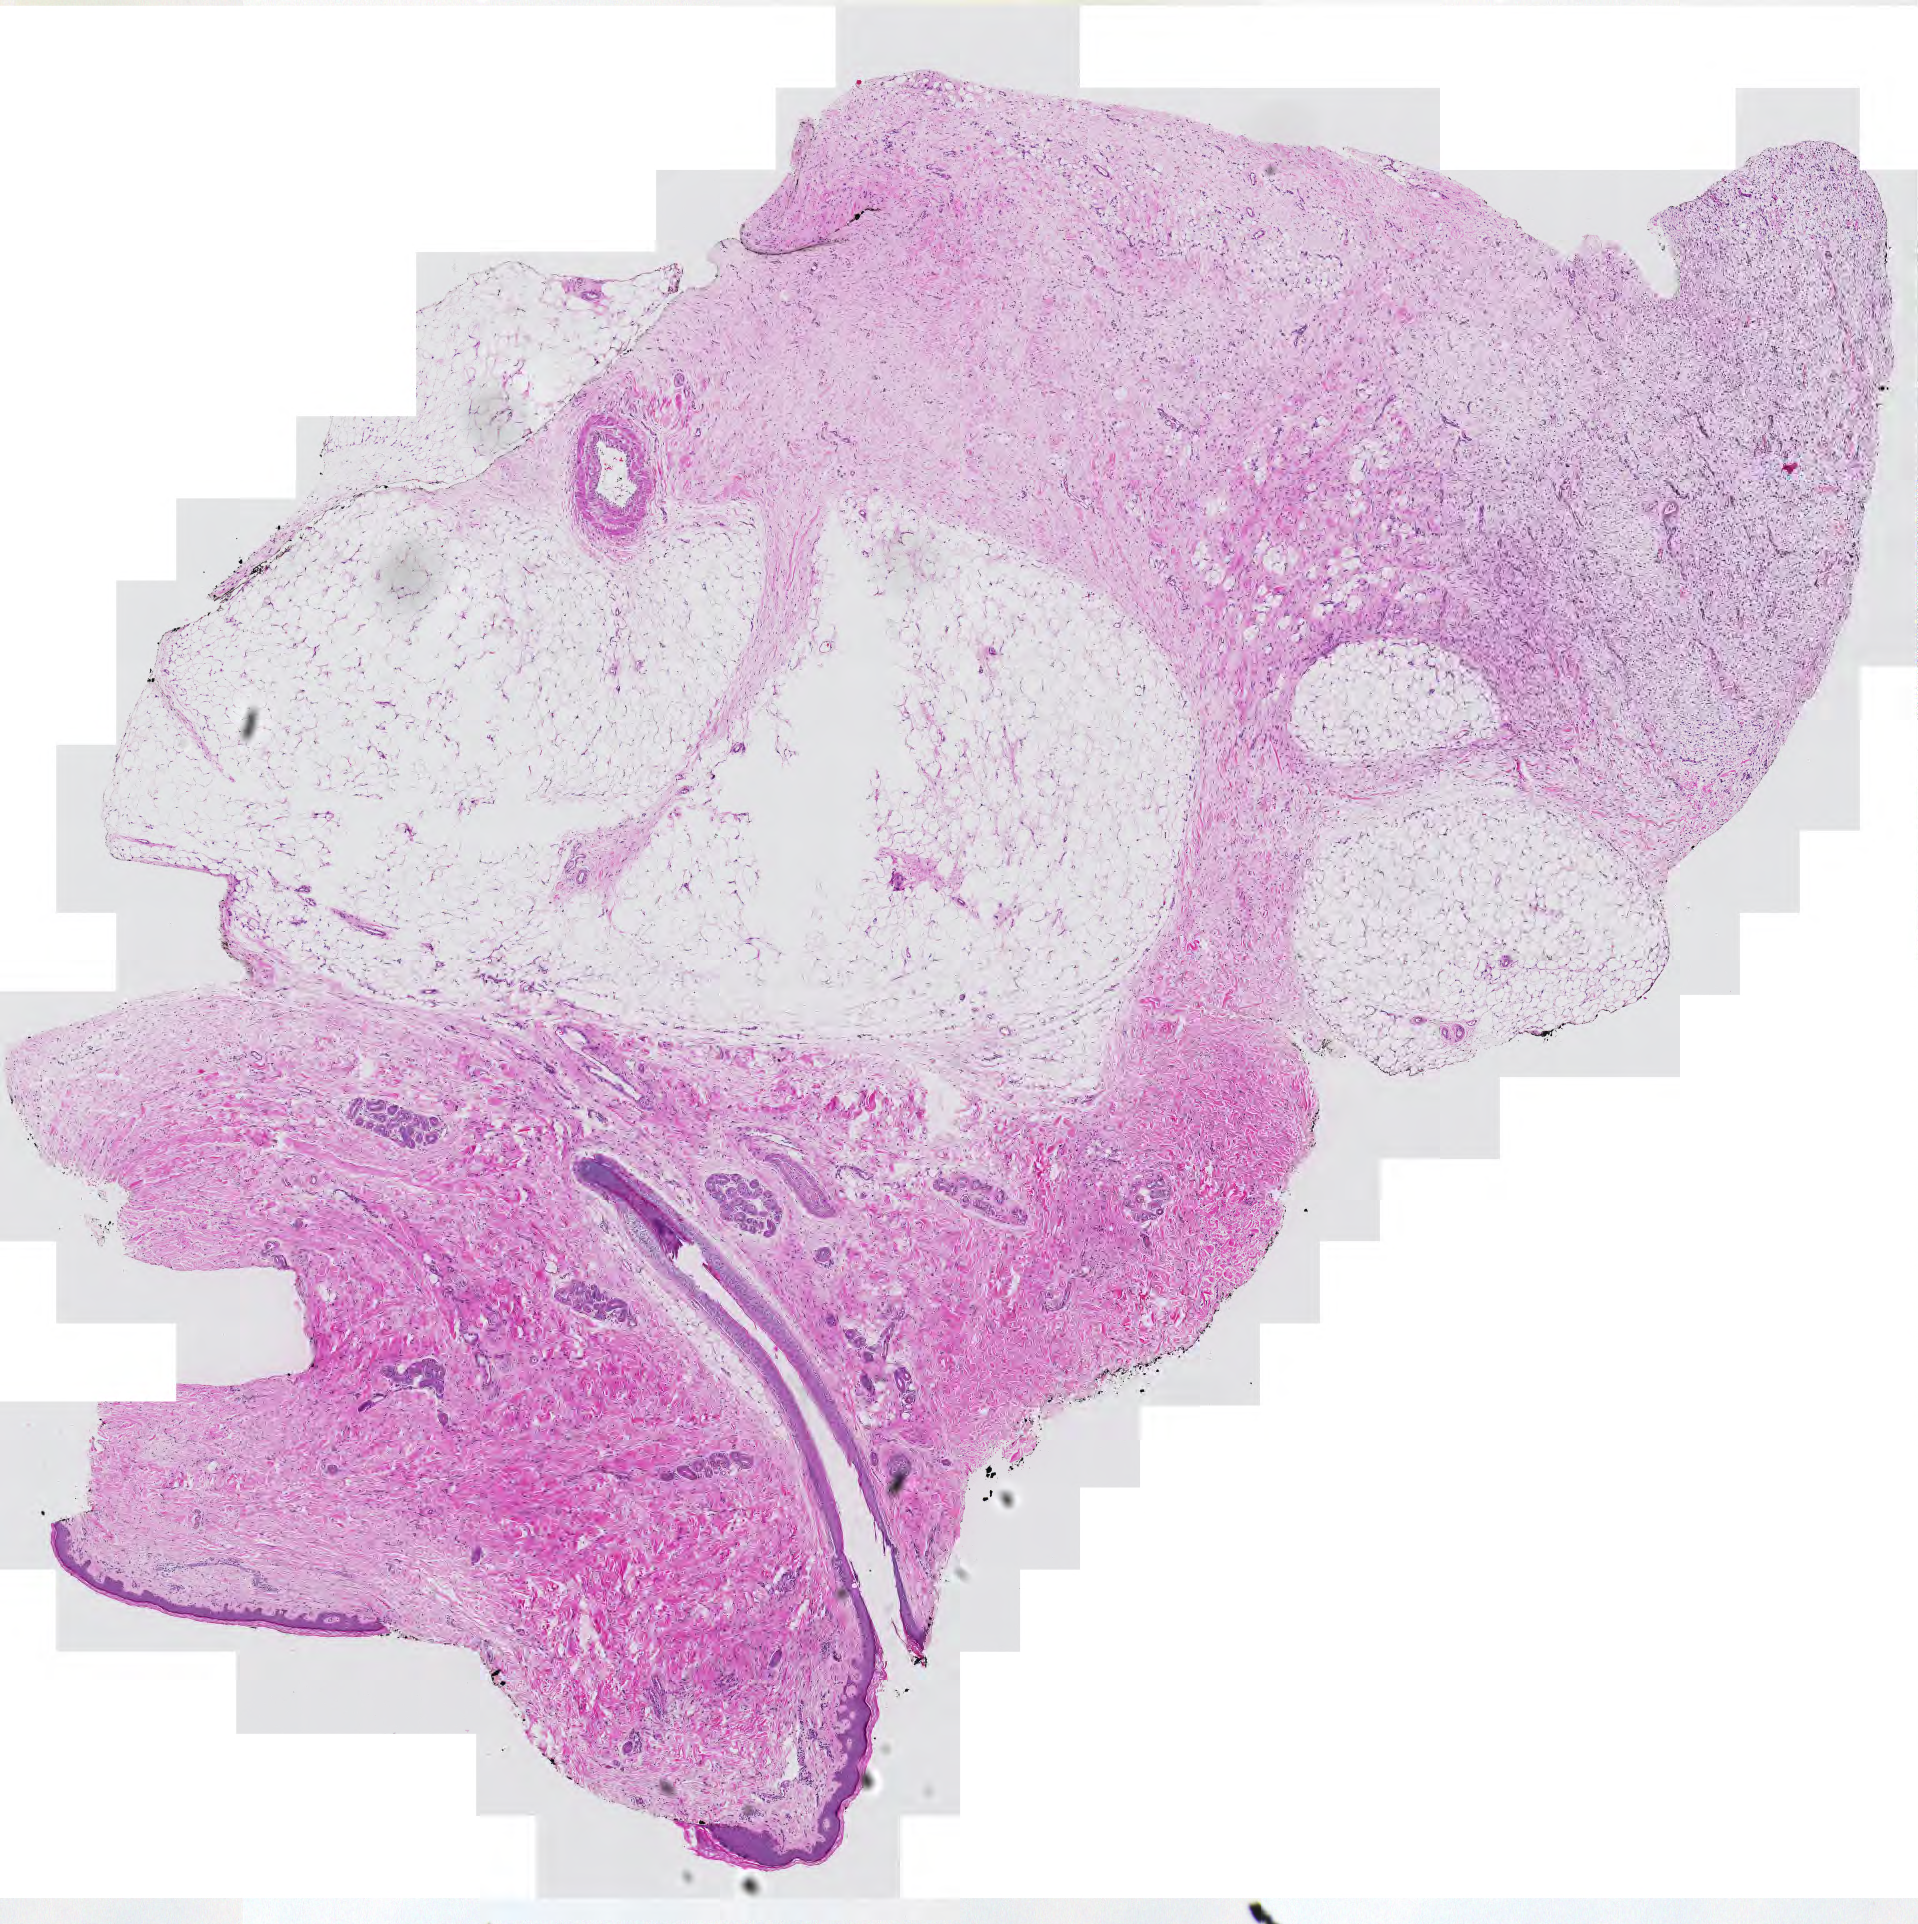
Digitized Hematoxylin and eosin (H&E) stained tissue section (whole slide), a low-resolution overview of the entire scanned area, about 9.9 x 9.9 mm (from a 20x scan). Tumour tissue sample. Female, 72 y/o.
• patient diagnosis (cohort enrolment): sarcoma (site not recorded at cohort level)